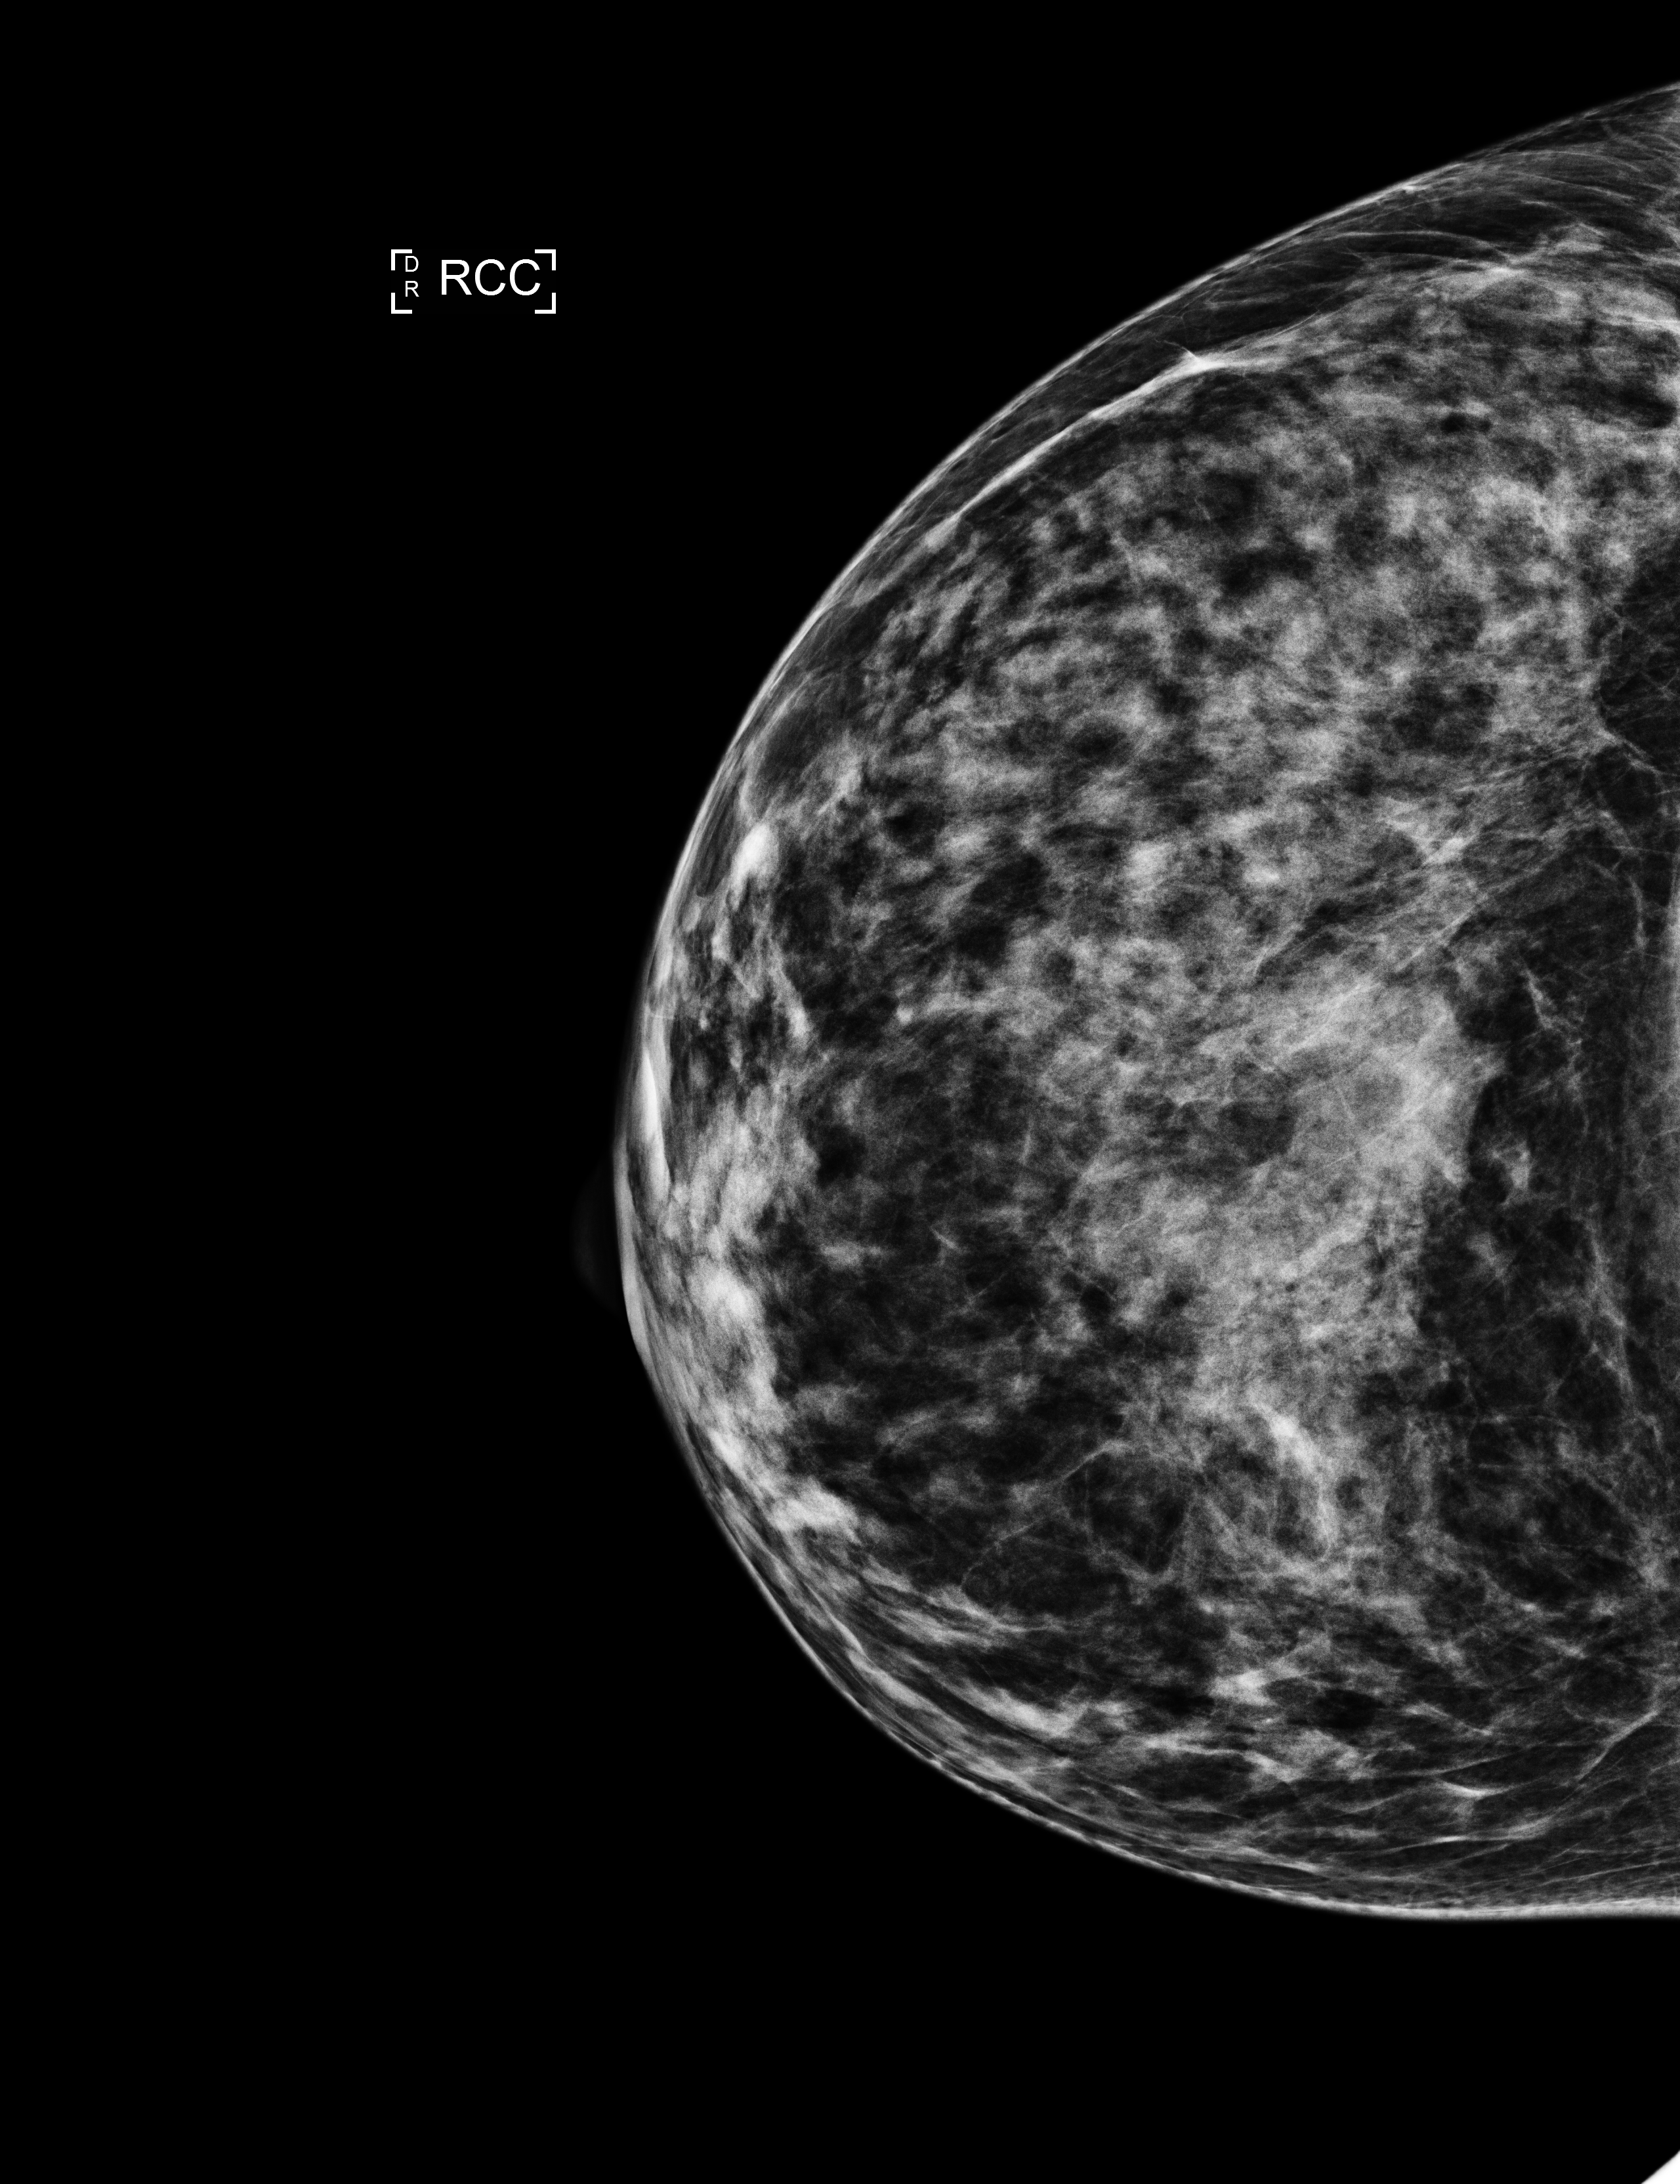
Digital mammogram (FFDM), right breast, craniocaudal (CC) view, screening examination, compressed breast thickness 54 mm. Female patient, age 44 years.
BI-RADS breast density category at the screening exam (both breasts, scale 1–4): 4. Final BI-RADS category for the screening round (tomosynthesis exam, both breasts): category 1. Recall: no recall after this screen.